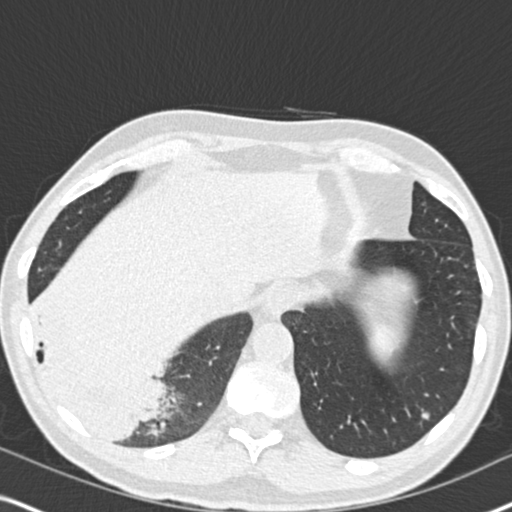
Low-dose screening chest CT, axial slice, second screening round (one year after baseline), lung window (W 1500 / L -600 HU), slice 132 of 182 in the series. Male, age 61 years at enrolment. Current smoker at enrolment.
• Expert-annotated lung lesion, bounding box [x1, y1, x2, y2] px = [18, 278, 180, 454].
• The exam's reader record, not a measurement of the box and not confirmed to be the same lesion: non-calcified nodule or mass ≥4 mm, right lower lobe, 90 × 80 mm, soft tissue attenuation, pre-existing on the prior screen: yes; interval growth: yes.
• Lung cancer was diagnosed 20 days after this screen: bronchiolo-alveolar adenocarcinoma, NOS, right lower lobe, moderately differentiated (G2), stage IIIB (AJCC 6th edition), 90 mm at pathology.